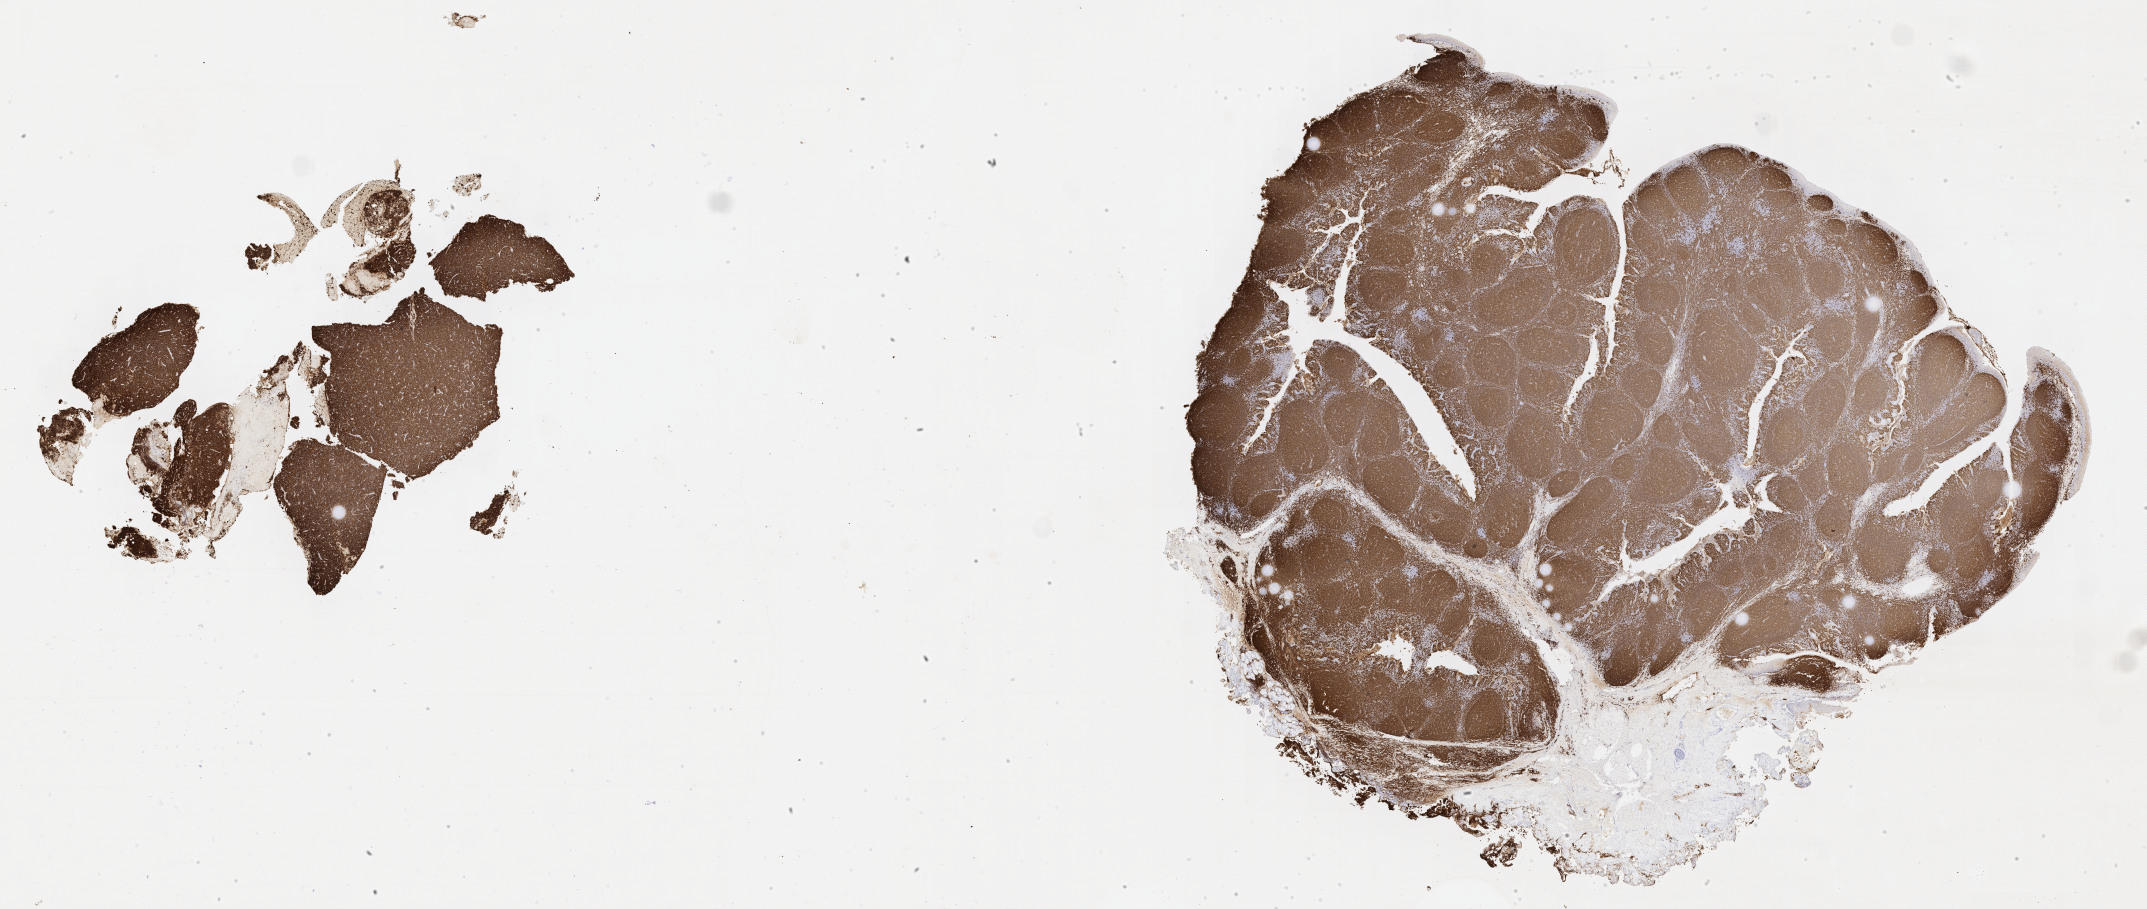
IHC for CD20, whole-slide image — whole scanned area (about 34.7 x 14.7 mm) shown as a low-resolution overview; tumor tissue; site: lymph node. Female patient, 71 years old.
Diagnosis: Diffuse large B-cell lymphoma, NOS.